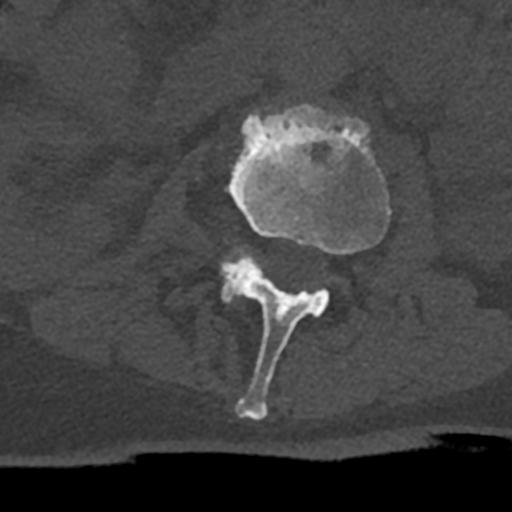
CT including the spine, one axial slice; 120 kVp; bone window (W 1800 / L 400 HU); 0.5 mm slice thickness; 512 × 512 image matrix, field of view 160 × 160 mm. Male patient, age 74 years. From the clinical record (not read from this slice): primary cancer: renal; vertebrae with lytic lesions (as recorded): T10, L1, L2, L3, L4, L5.
Structures marked on this image (semi-automatically segmented with operator editing):
- L2 vertebra: box from (x=228, y=104) to (x=391, y=420) px
- L3 vertebra: (x=222, y=248)–(x=260, y=303)